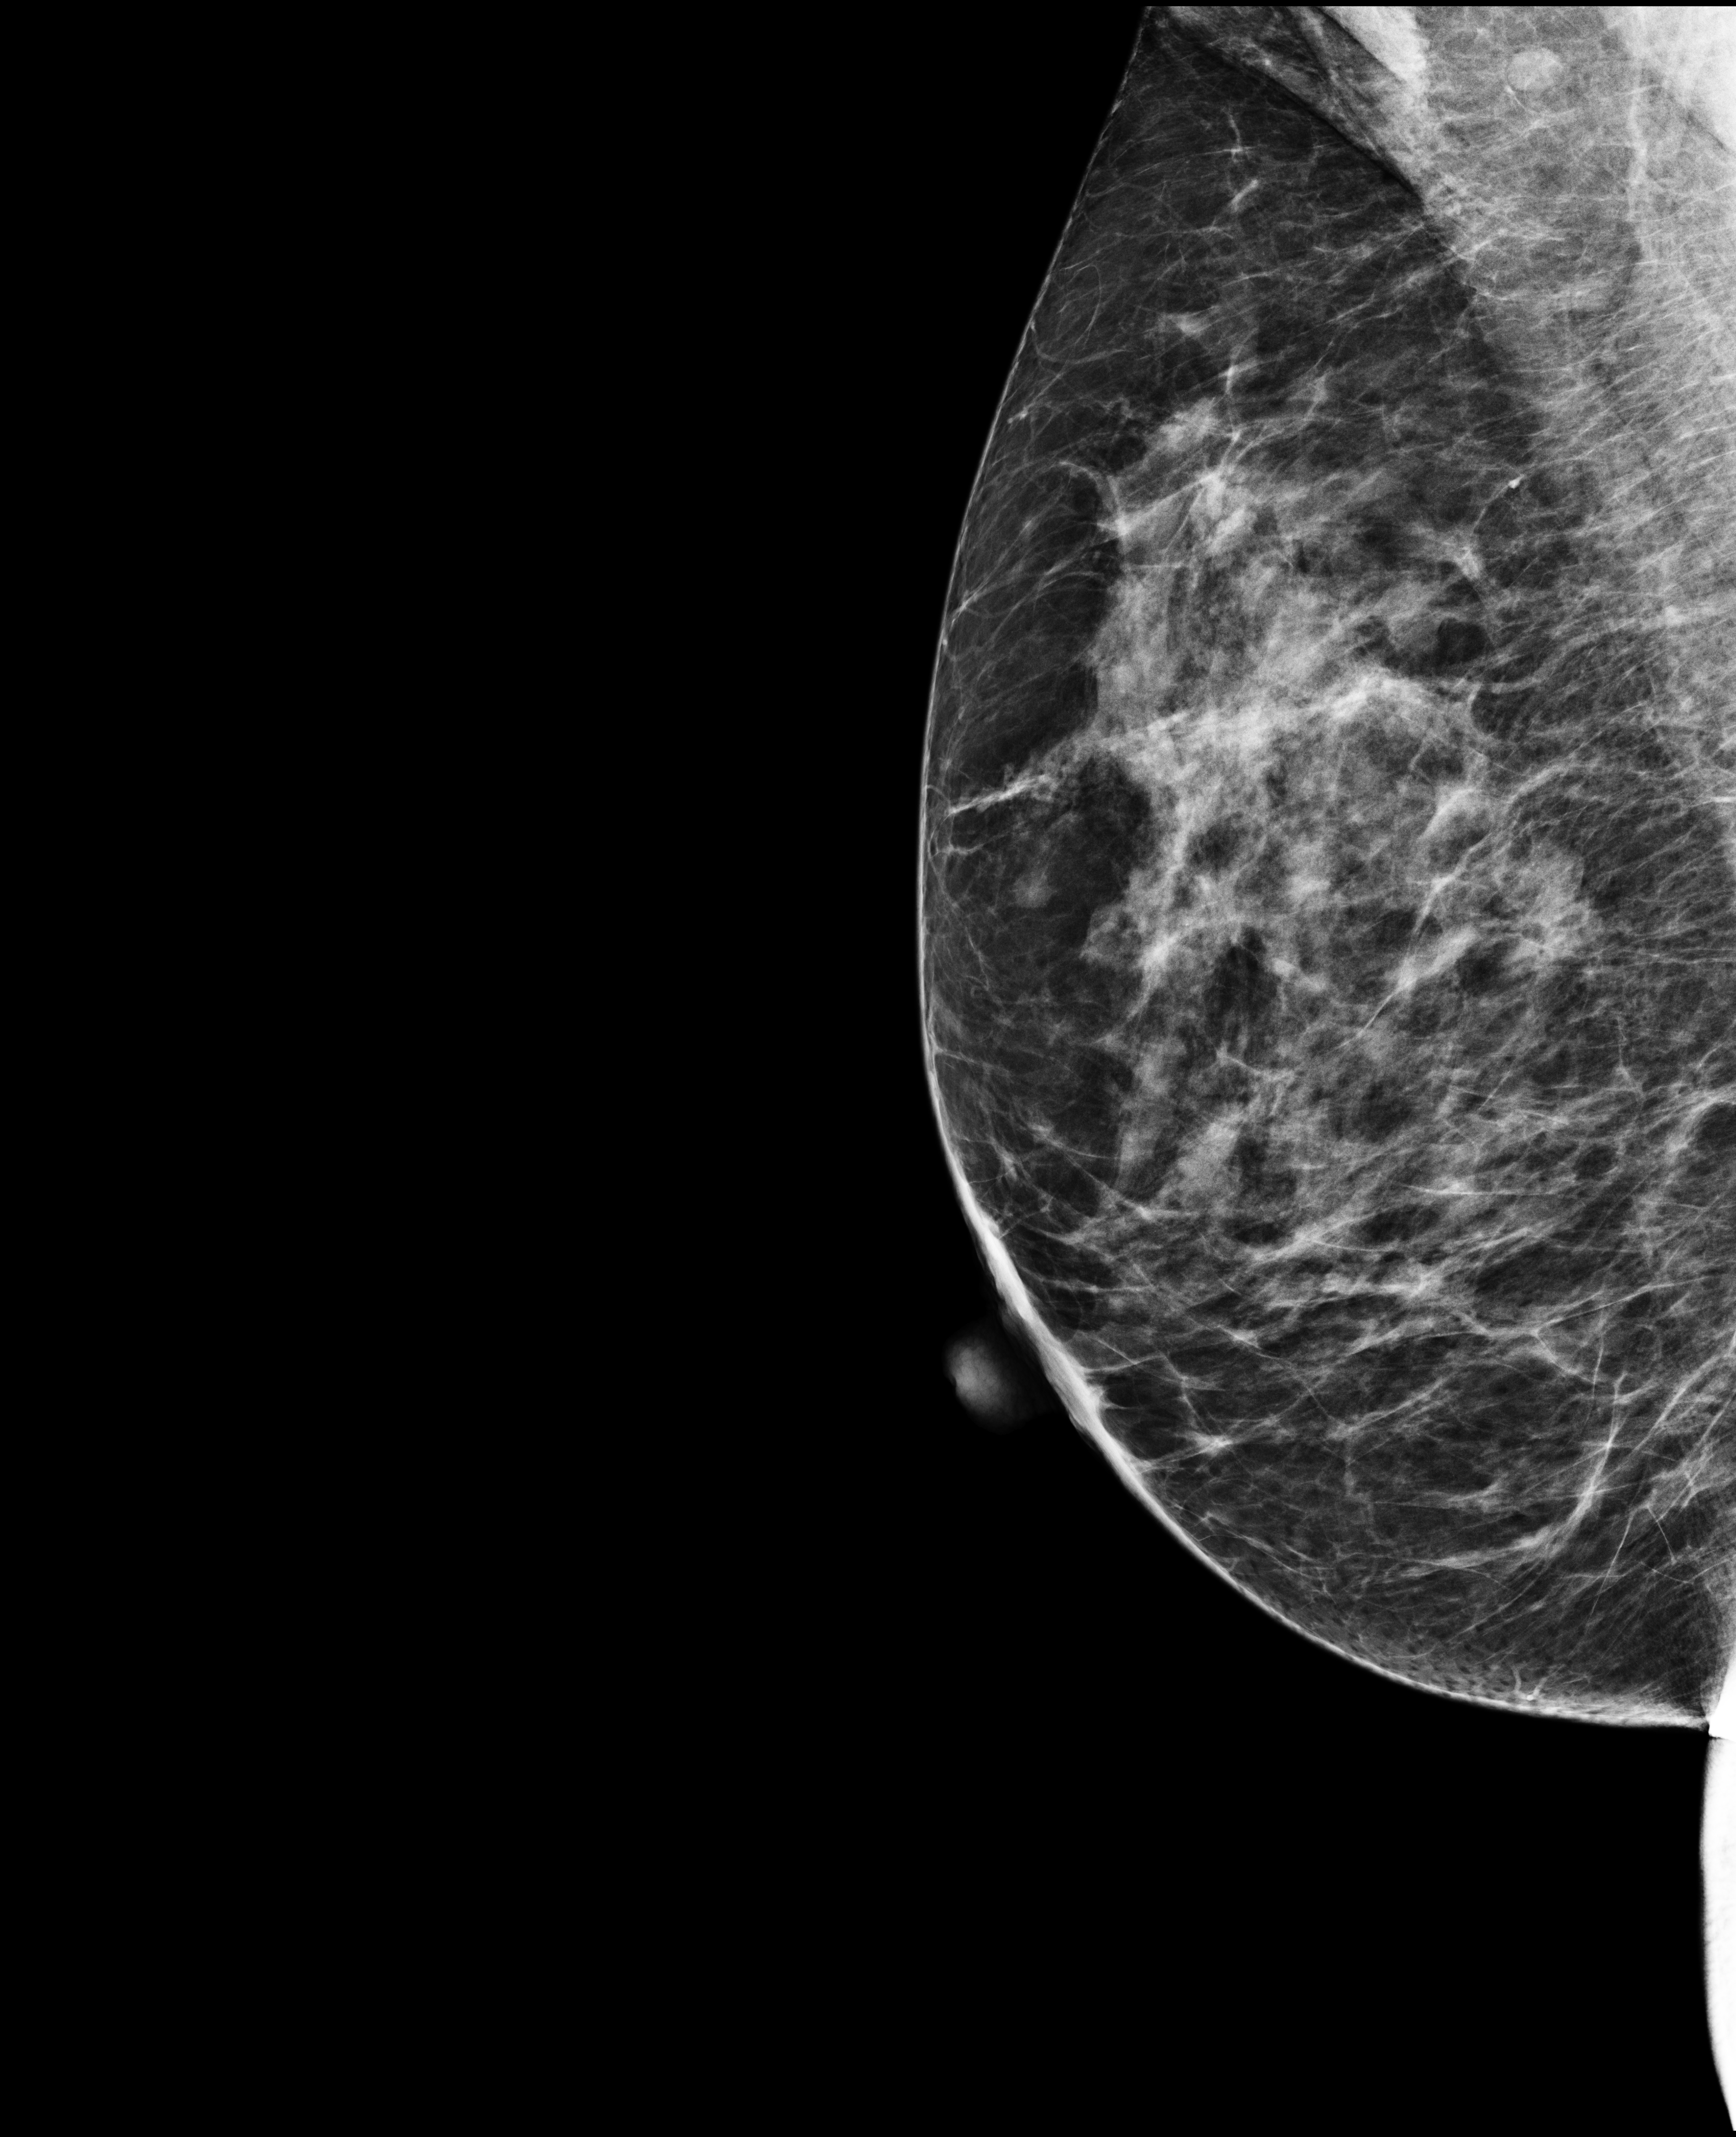
Annual screening mammography examination, compressed breast thickness 62 mm.
Image type: full-field digital mammogram. Breast: right. Projection: MLO view.